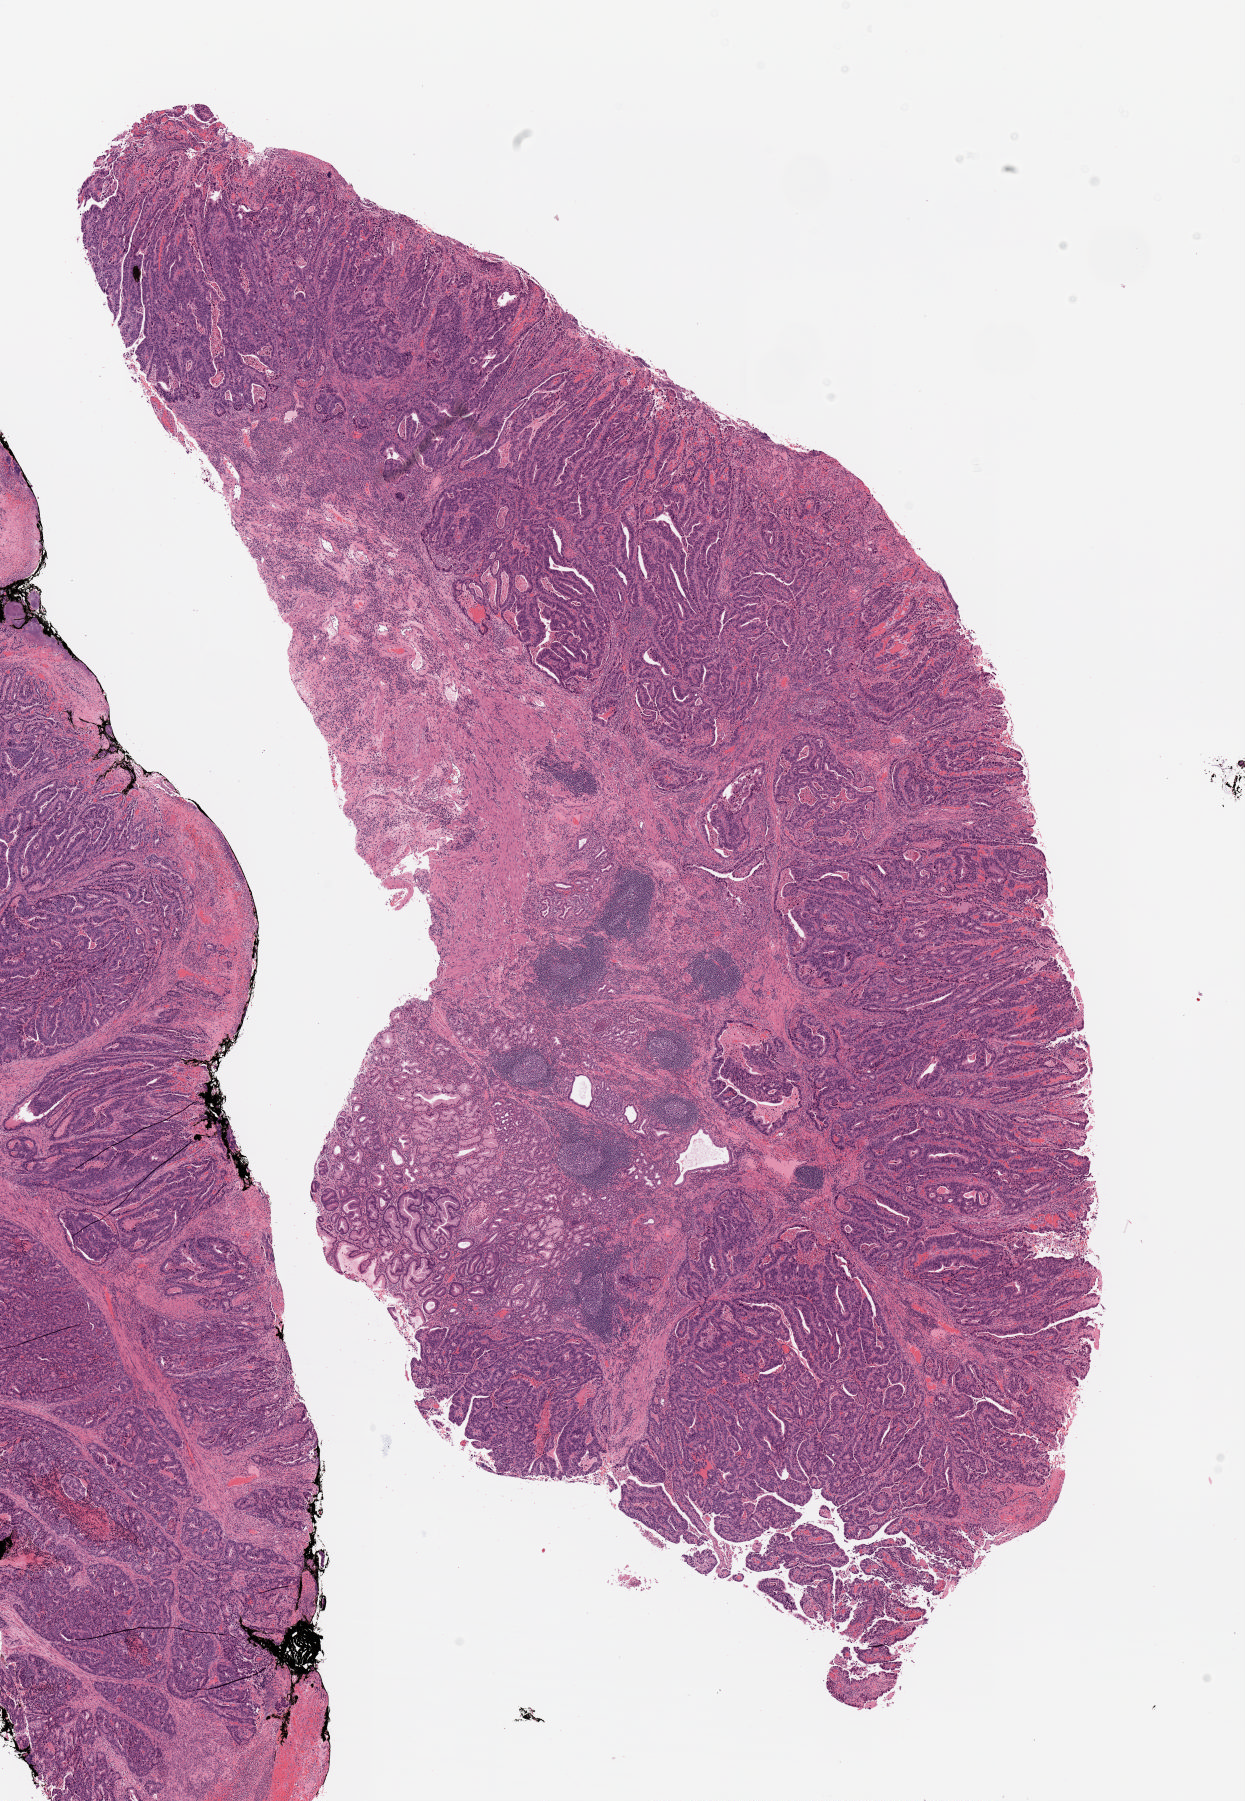
Whole-slide histology image, H&E-stained, whole scanned area (about 9.9 x 14.3 mm, slide scanned at 20x) shown as a low-resolution overview. Formalin-fixed paraffin-embedded (FFPE) diagnostic section. Primary tumour sample from the stomach. Female patient; age at initial diagnosis 79 years. Histologic grade: G1 (well differentiated).
- AJCC pathologic stage: IIB (7th edition)
- histologic diagnosis: Tubular adenocarcinoma (body of stomach)